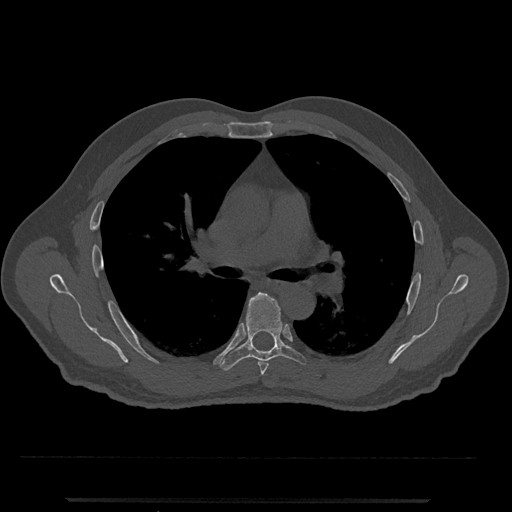
CT including the spine, one axial slice; position 750 of 797 along the scan axis; 120 kVp; bone window (W 1800 / L 400 HU); 0.5 mm slice thickness; 512 × 512 image matrix. Patient: male, 63 years. Case-level facts recorded for this patient, not image findings: primary cancer: prostate.
Outlined on this slice (semi-automatically segmented with operator editing):
- T5 vertebra: bounding box <258,361,269,375> (left, top, right, bottom; pixels)
- T6 vertebra: <220,292,306,371>